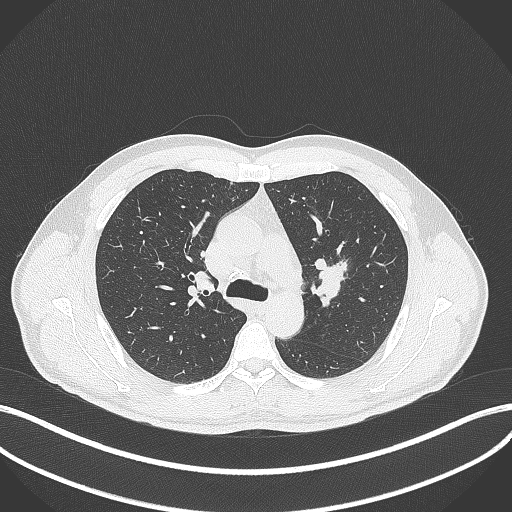
Chest CT, one axial slice. Slice 282 of 392 in the series (ordered by position). Reconstruction kernel B70f. 120 kVp. Lung window (W 1500 / L -600 HU). 512 × 512 image matrix. Male patient, age 50 years. Case-level facts recorded for this patient, not image findings: clinical TNM (as recorded): T1c N1 M1b.
Annotated regions visible in this slice (bounding box drawn by a radiologist):
- lung tumour (recorded histology: squamous cell carcinoma): bounding box [x1, y1, x2, y2] px = [310, 257, 351, 308]